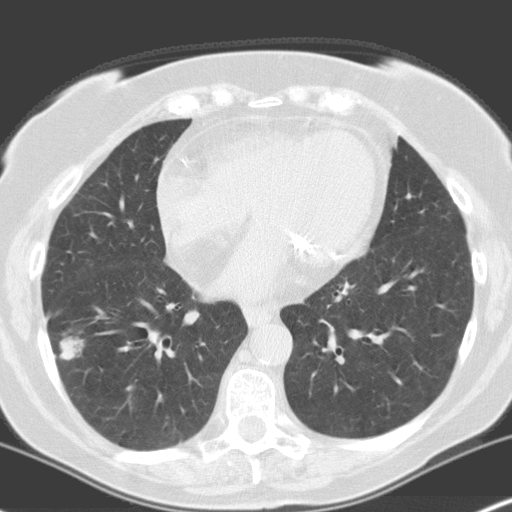
Low-dose screening chest CT, one axial slice; position 73 of 160 along the scan axis; 120 kVp; lung window (W 1500 / L -600 HU); 512 × 512 image matrix.
Structures marked on this image (expert manual segmentation):
- lesion 1 (tumor, lower lobe of right lung): bounding box (x1, y1, x2, y2) in pixels: (60, 336, 84, 360)